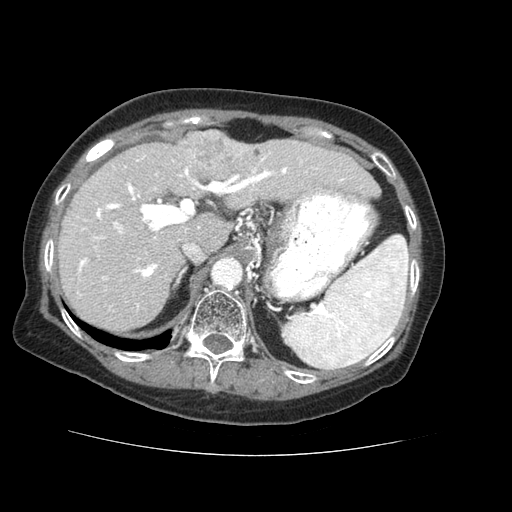
Contrast-enhanced abdominal CT (liver protocol), one axial slice; position 42 of 73 along the scan axis; 120 kVp; soft-tissue window (W 400 / L 40 HU); 2.5 mm slice thickness; 512 × 512 image matrix, field of view 360 × 360 mm. From the clinical record (not read from this slice): diagnosis: hepatocellular carcinoma (patient treated with transarterial chemoembolisation; whether this scan precedes or follows treatment is not stated here); TNM stage (as recorded): Stage-IVB; Child-Pugh class: A; tumour differentiation: well differentiated; tumour nodularity: uninodular.
Outlined on this slice (semi-automatically segmented with operator editing):
- liver parenchyma outside the tumour (the mass and vessels are separate outlines, so this box may not span the whole liver): bounding box <56,130,380,332> (left, top, right, bottom; pixels)
- mass: <181,129,247,180>
- liver vessels: <78,152,345,308>